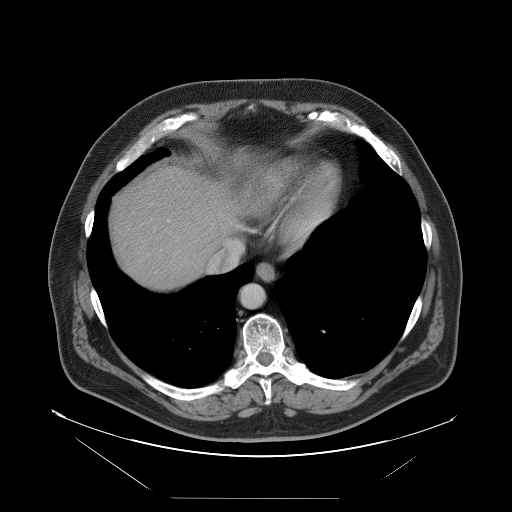
Contrast-enhanced abdominal CT, one axial slice; slice 90 of 114 in the series (ordered by position); 120 kVp; intravenous contrast given; soft-tissue window (W 400 / L 40 HU); 5 mm slice thickness; 512 × 512 image matrix, field of view 500 × 500 mm. Male patient, age 61 years. From the clinical record (not read from this slice): diagnosis: colorectal cancer liver metastases, imaged before liver resection.
Annotated regions visible in this slice (outlined manually by an expert reader):
- hepatic veins: bounding box [x1, y1, x2, y2] px = [208, 240, 243, 272]
- liver: [110, 167, 240, 290]
- planned liver remnant (the part of the liver to remain after resection): [160, 168, 241, 250]